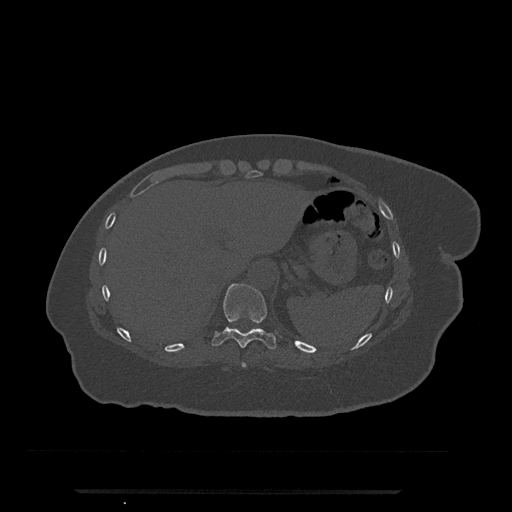
CT including the spine, one axial slice. Position 285 of 797 along the scan axis. 120 kVp. Bone window (W 1800 / L 400 HU). 512 × 512 image matrix, field of view 440 × 440 mm. Patient: female, 51 years. From the clinical record (not read from this slice): primary cancer: neuro; vertebrae with lytic lesions (as recorded): T8.
Outlined on this slice (semi-automatic segmentation, software-assisted and operator-edited):
- T10 vertebra: bounding box <212,283,277,350> (left, top, right, bottom; pixels)
- T9 vertebra: <242,362,247,368>